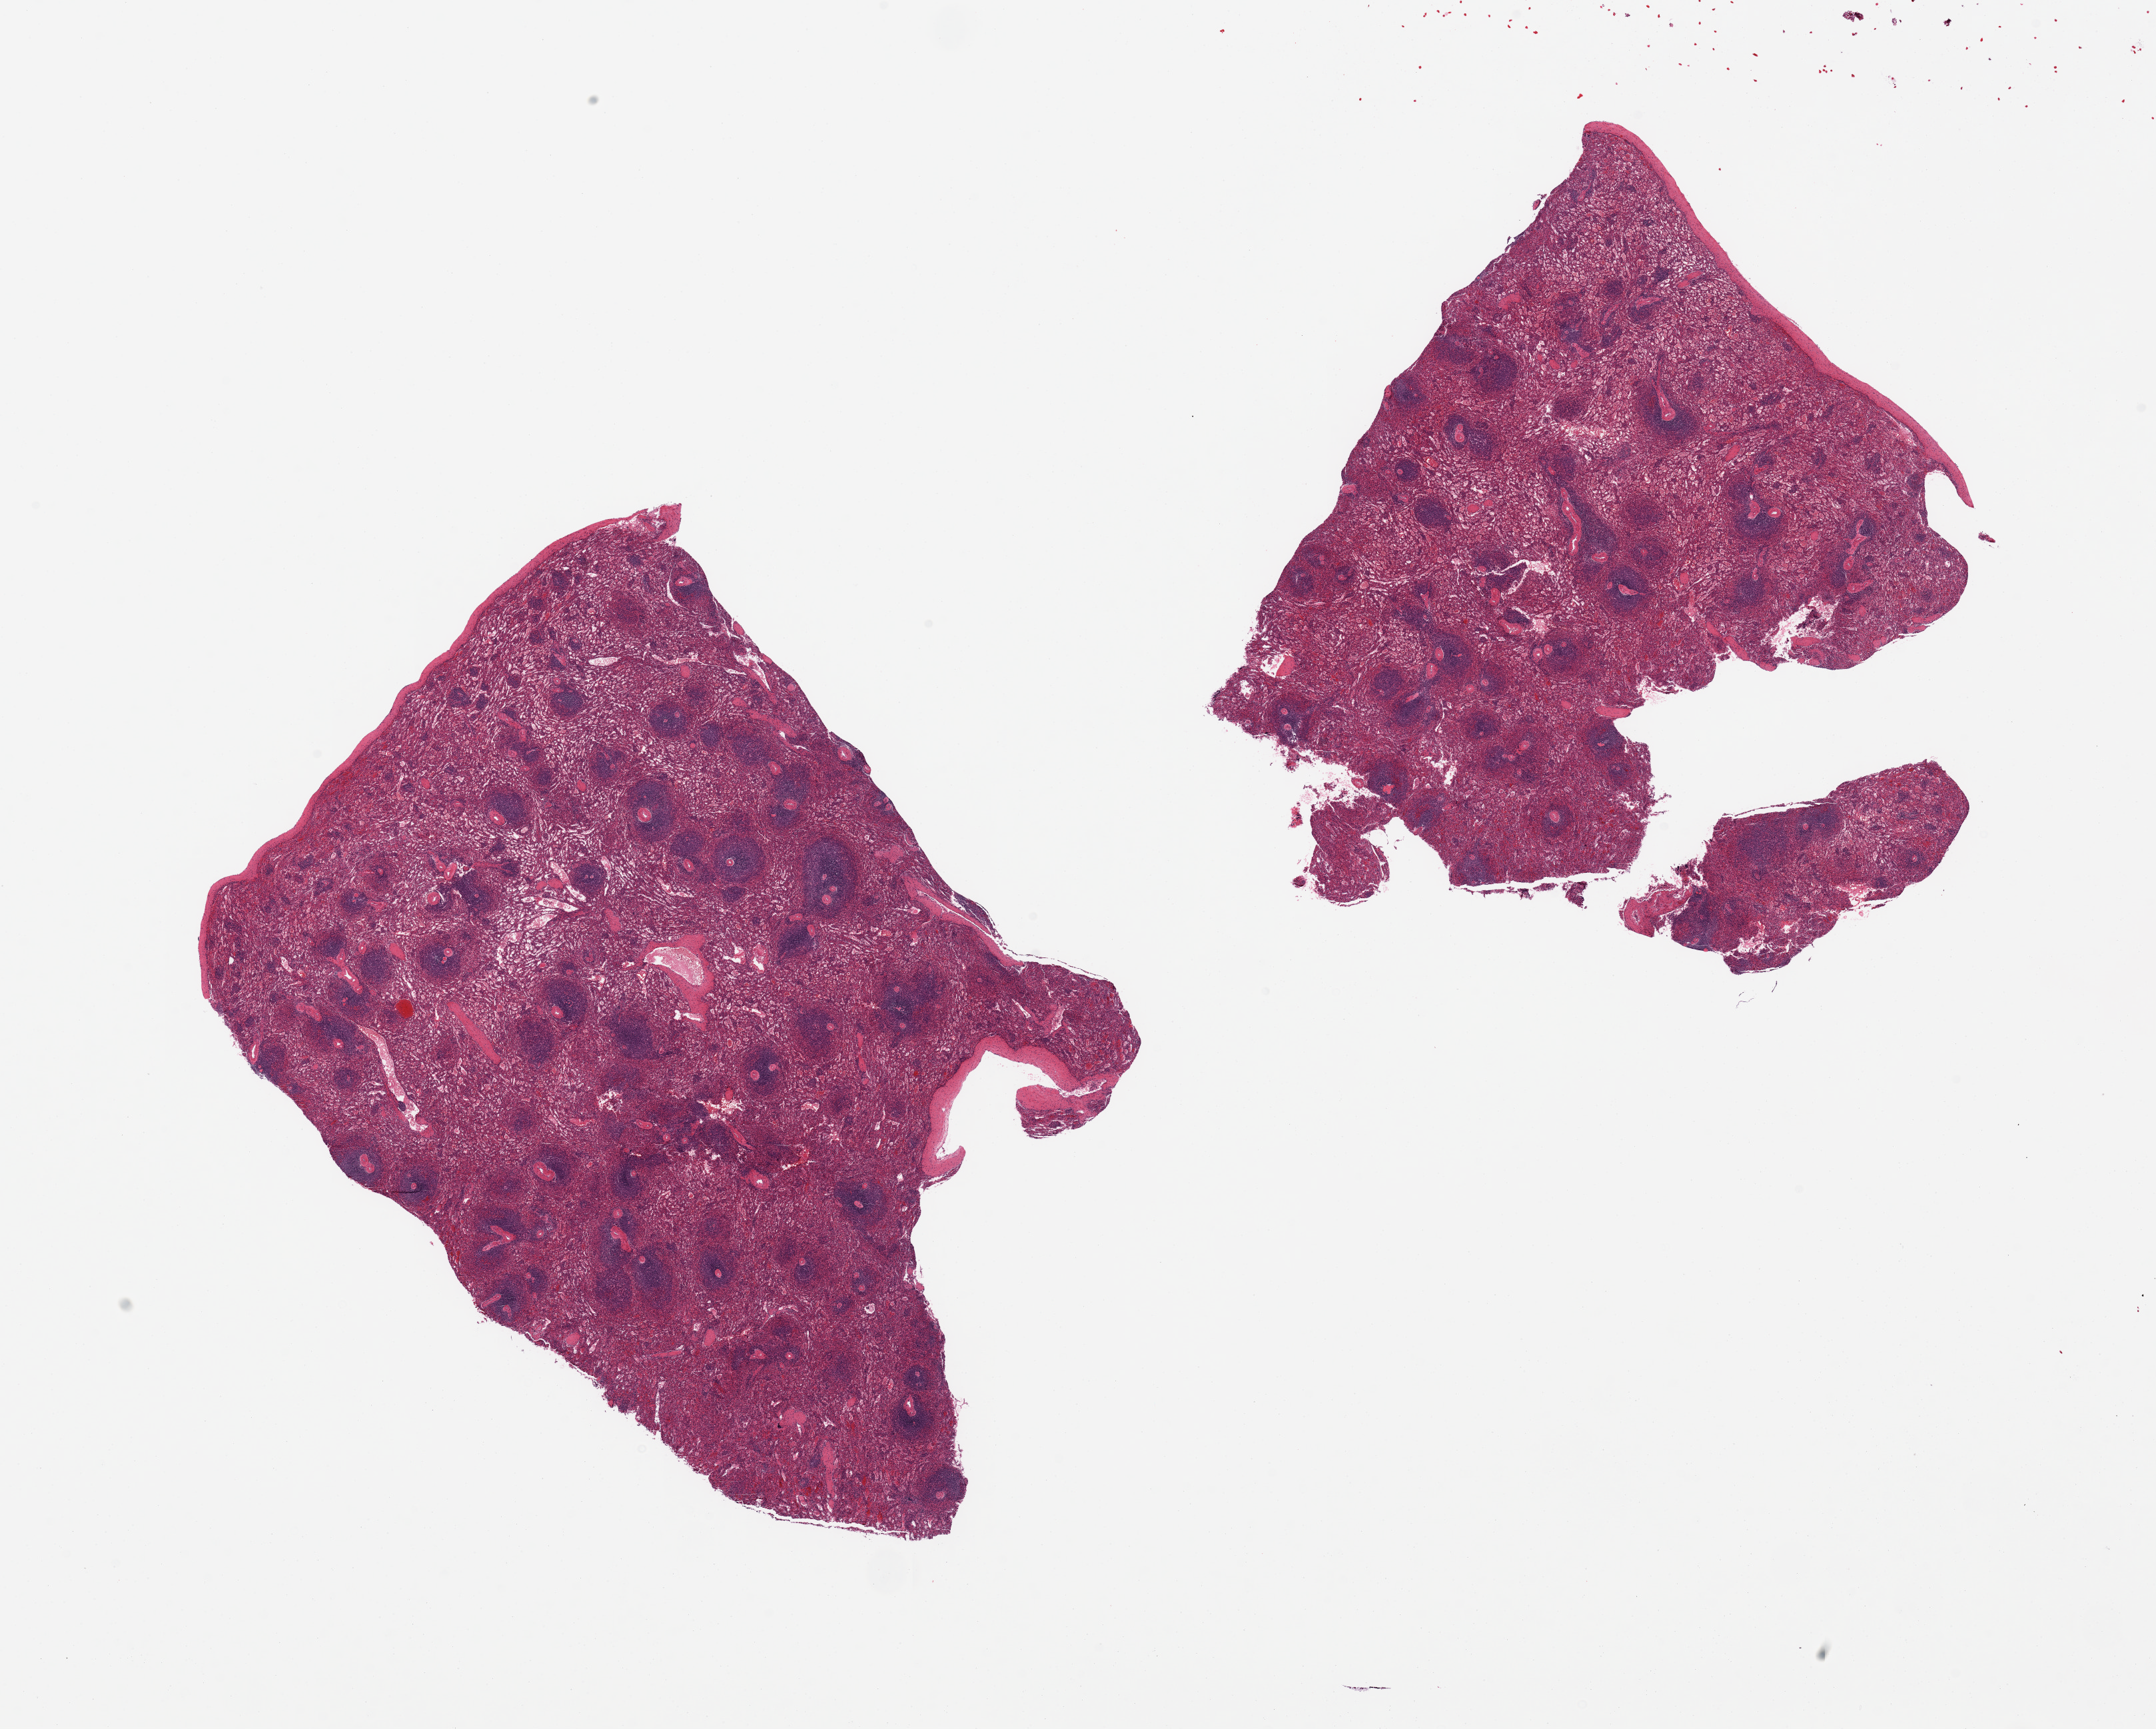
Hematoxylin and eosin (H&E) whole-slide image — a low-resolution overview of the entire scanned area, about 25.6 x 20.5 mm (acquisition: 20x scan), PAXgene-fixed, paraffin-embedded tissue, target tissue: spleen, donor tissue sample. Female donor.
- review note (as recorded): 2 pieces, no abnormalities